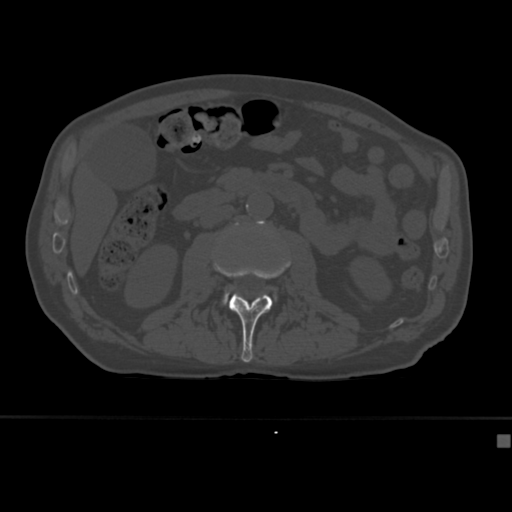
CT including the spine, one axial slice; position 142 of 430 along the scan axis; bone window (W 1800 / L 400 HU); 512 × 512 image matrix. Patient: male, 64 years. From the clinical record (not read from this slice): primary cancer: uterus; vertebrae with lytic lesions (as recorded): T1, T4, T5, T7, L5.
Annotated regions visible in this slice (semi-automatic segmentation, software-assisted and operator-edited):
- L2 vertebra: bounding box [x1, y1, x2, y2] px = [214, 259, 291, 363]
- L3 vertebra: [223, 220, 276, 305]